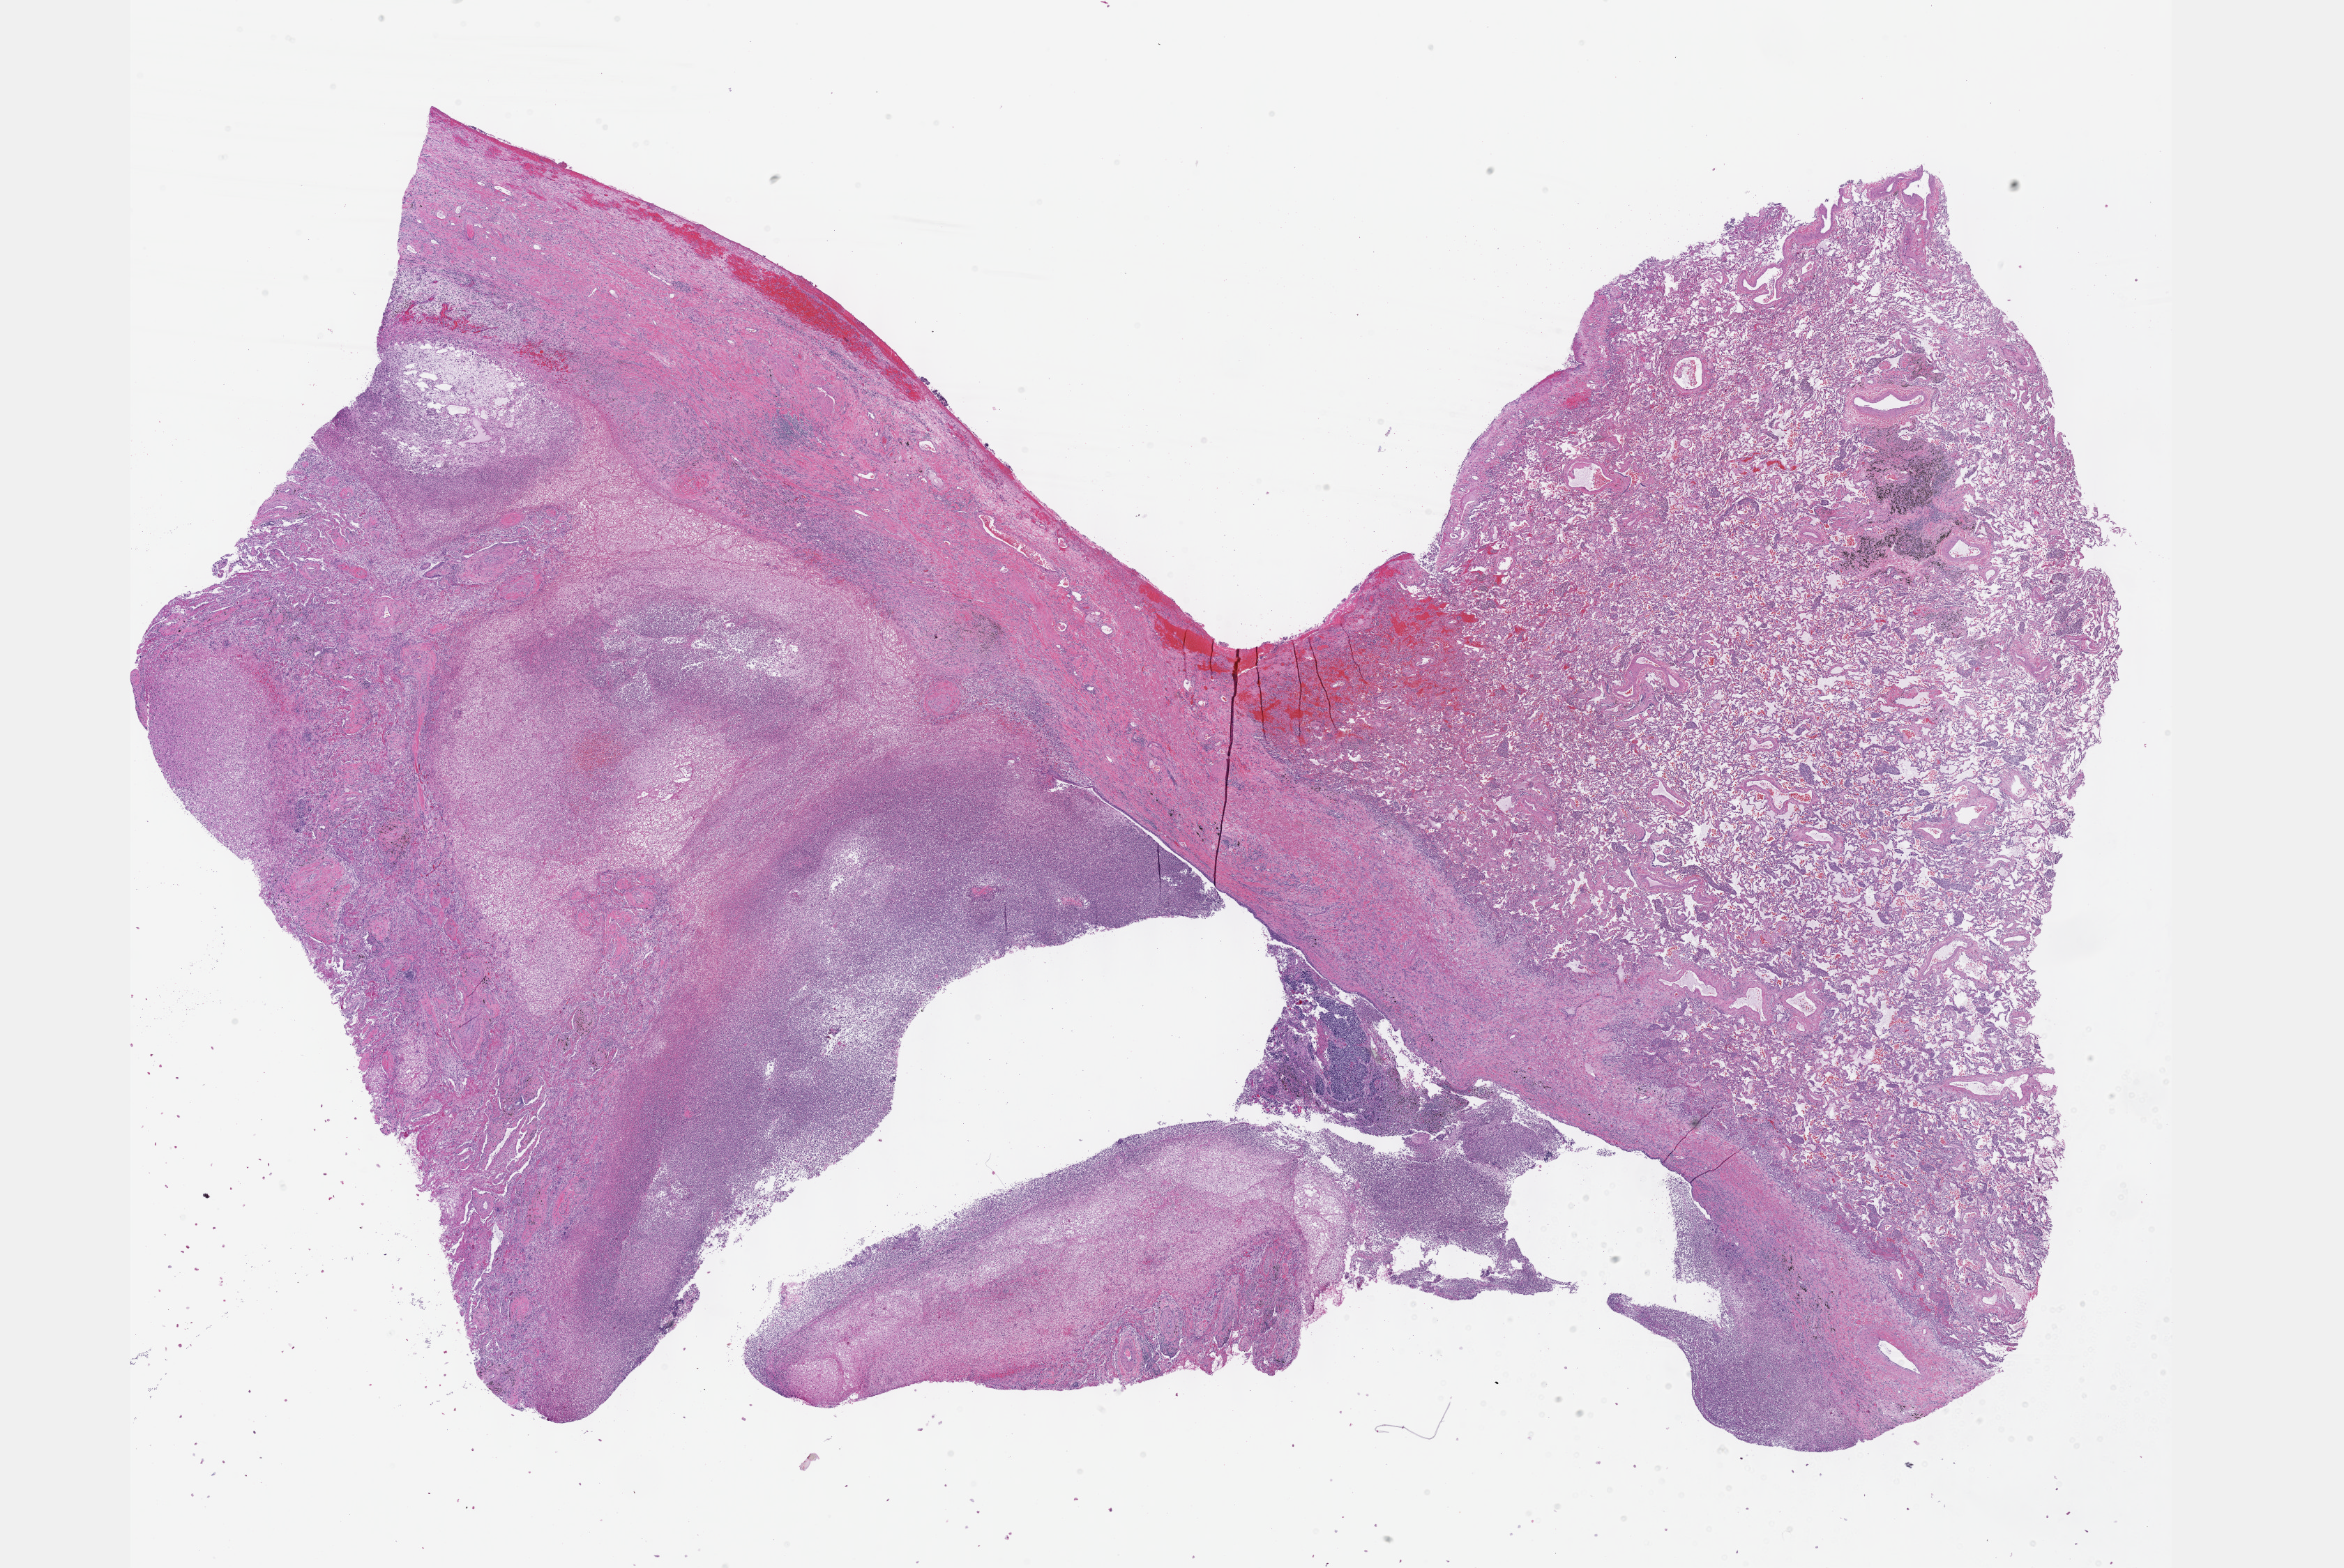
H&E whole-slide image — low-resolution overview of the scanned area, about 27.2 x 18.2 mm (acquisition: 40x scan), FFPE section, lung, primary tumour sample. Patient: male, age at initial diagnosis 71 years.
- AJCC pathologic stage: IIIA (7th edition)
- TNM: T3 N1 MX
- diagnosis: Squamous cell carcinoma, NOS
- laterality: left